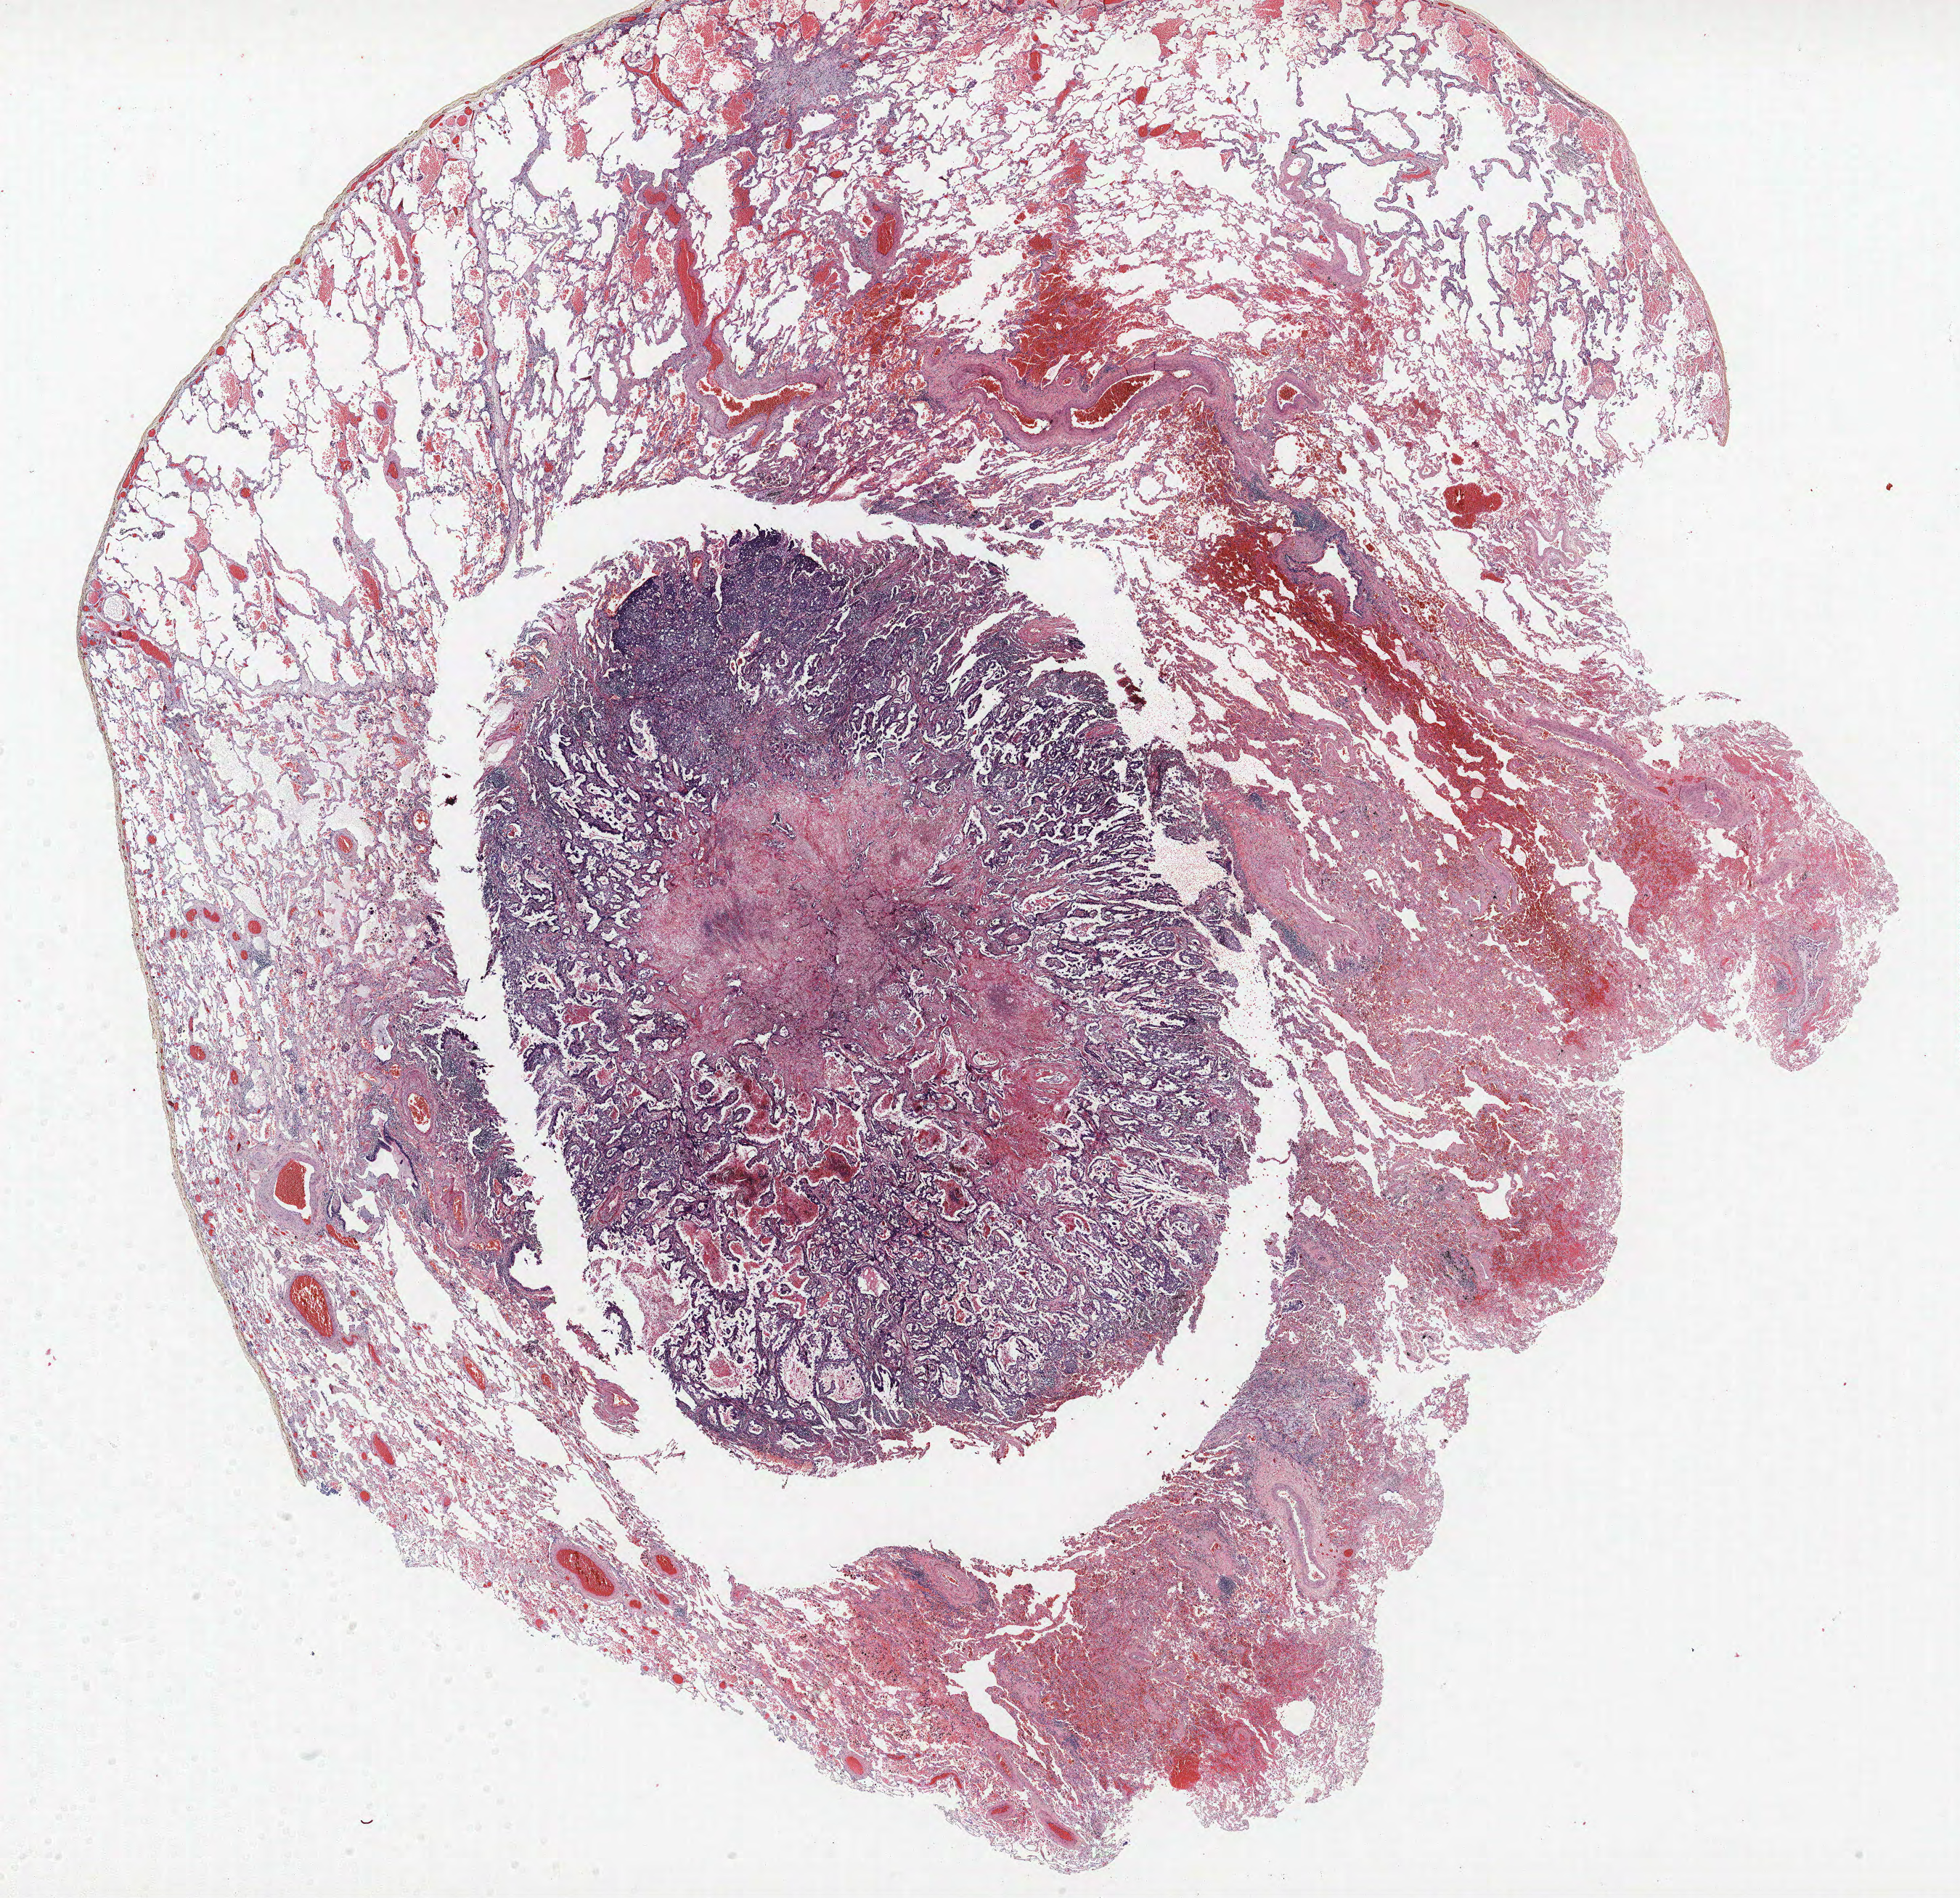
H&E-stained whole-slide image, shown as a low-resolution overview of the whole scanned area (about 21.6 x 20.9 mm, slide scanned at 40x), formalin-fixed paraffin-embedded (FFPE) section, lung. Male patient, aged 63 at enrolment. Current smoker at enrolment. Grade: moderately differentiated (G2).
ICD-O-3 topography: lower lobe of lung (C34.3). Primary tumour location (clinical record): right lower lobe. Tumour size (pathology): 12 mm. Participant's lung-cancer diagnosis: Adenocarcinoma, NOS. Stage (AJCC 6th edition): IA. Note: participant had 3 primary lung cancers recorded; fields above describe the first.